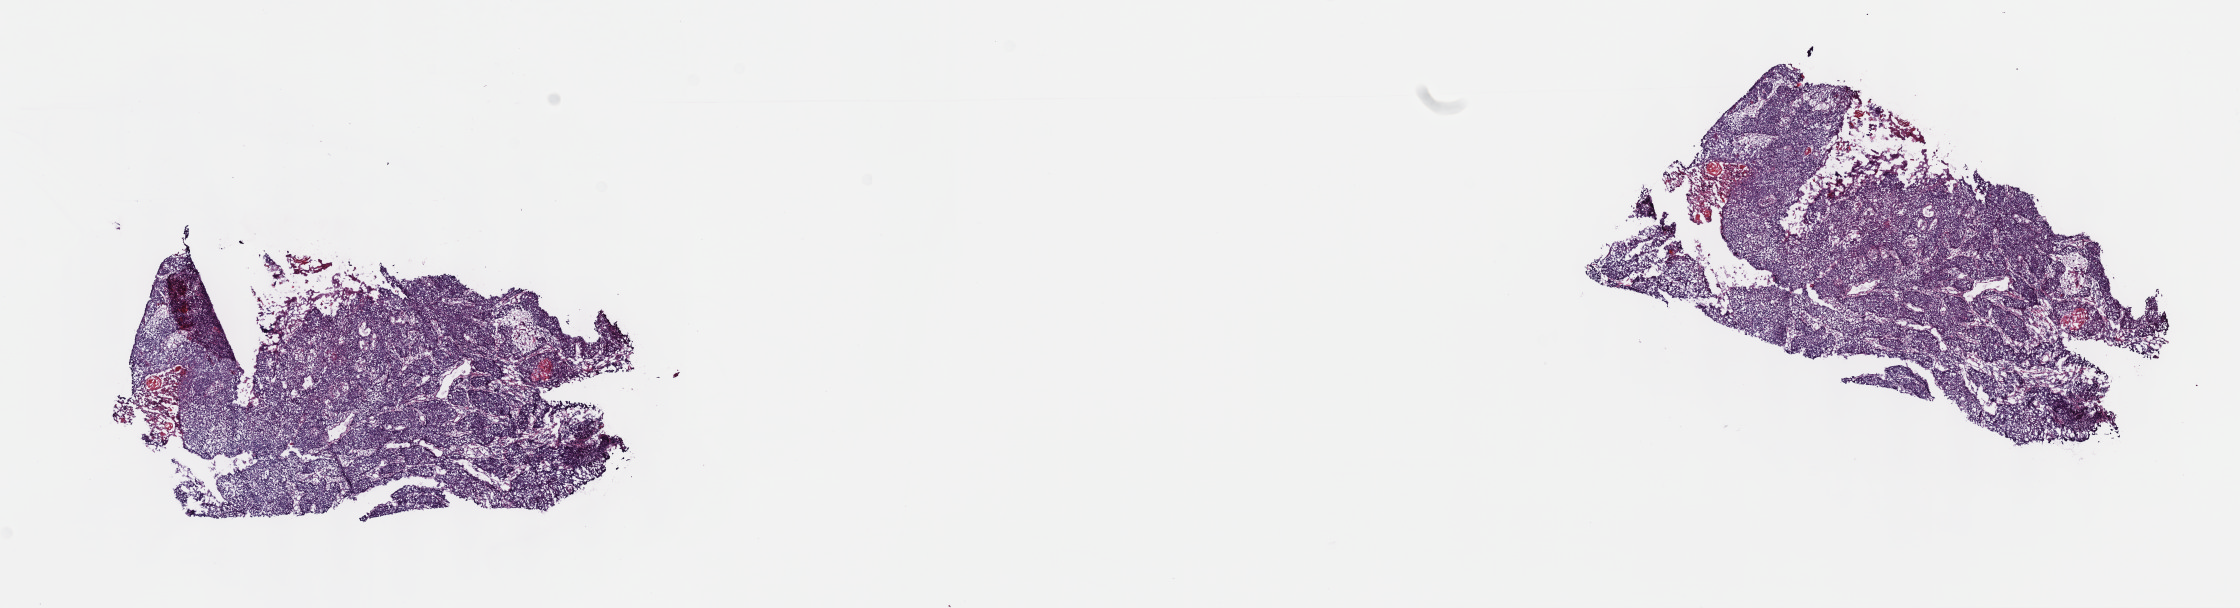
Whole-slide histology image, Hematoxylin and eosin (H&E) stained — a low-resolution overview of the entire scanned area, about 18.1 x 4.9 mm (slide scanned at 40x); frozen section from the top of the tissue portion; sample: primary tumour, esophagus. Male, age 42 years at initial diagnosis. Histologic grade: G2 (moderately differentiated). Pathologist review of this section (percent, as recorded): tumour cells 100%, tumour nuclei 80%, normal cells 0%, stromal cells 0%, necrosis 0%. Infiltration values recorded for this section: lymphocyte infiltration 3%, monocyte infiltration 0%, neutrophil infiltration 0%.
• AJCC pathologic stage: IIA (6th edition)
• pathologic diagnosis: Squamous cell carcinoma, NOS
• TNM: T2 N0 M0